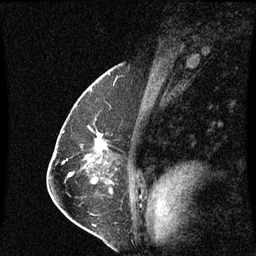
Breast MRI (dynamic contrast-enhanced), one sagittal slice. Slice 40 of 60 in the series (ordered by position). Dynamic contrast-enhanced series, image 2 of 3 at this slice position (ordered by acquisition). 1.5 T. TE 4.2 ms, TR 8.9 ms. 2 mm slice thickness. 256 × 256 image matrix. Patient: female, 57 years. From the clinical record (not read from this slice): setting: breast cancer imaged before/during neoadjuvant chemotherapy; receptor status: HR-positive, HER2-negative.
Outlined on this slice (semi-automatically segmented with operator editing):
- analysis volume of interest (the breast-tissue region the enhancement analysis was run in; not a lesion): bounding box <84,132,106,159> (left, top, right, bottom; pixels)
- tumour enhancement mask (voxels above the 70 % enhancement threshold inside the analysis volume of interest): <96,140,104,149>